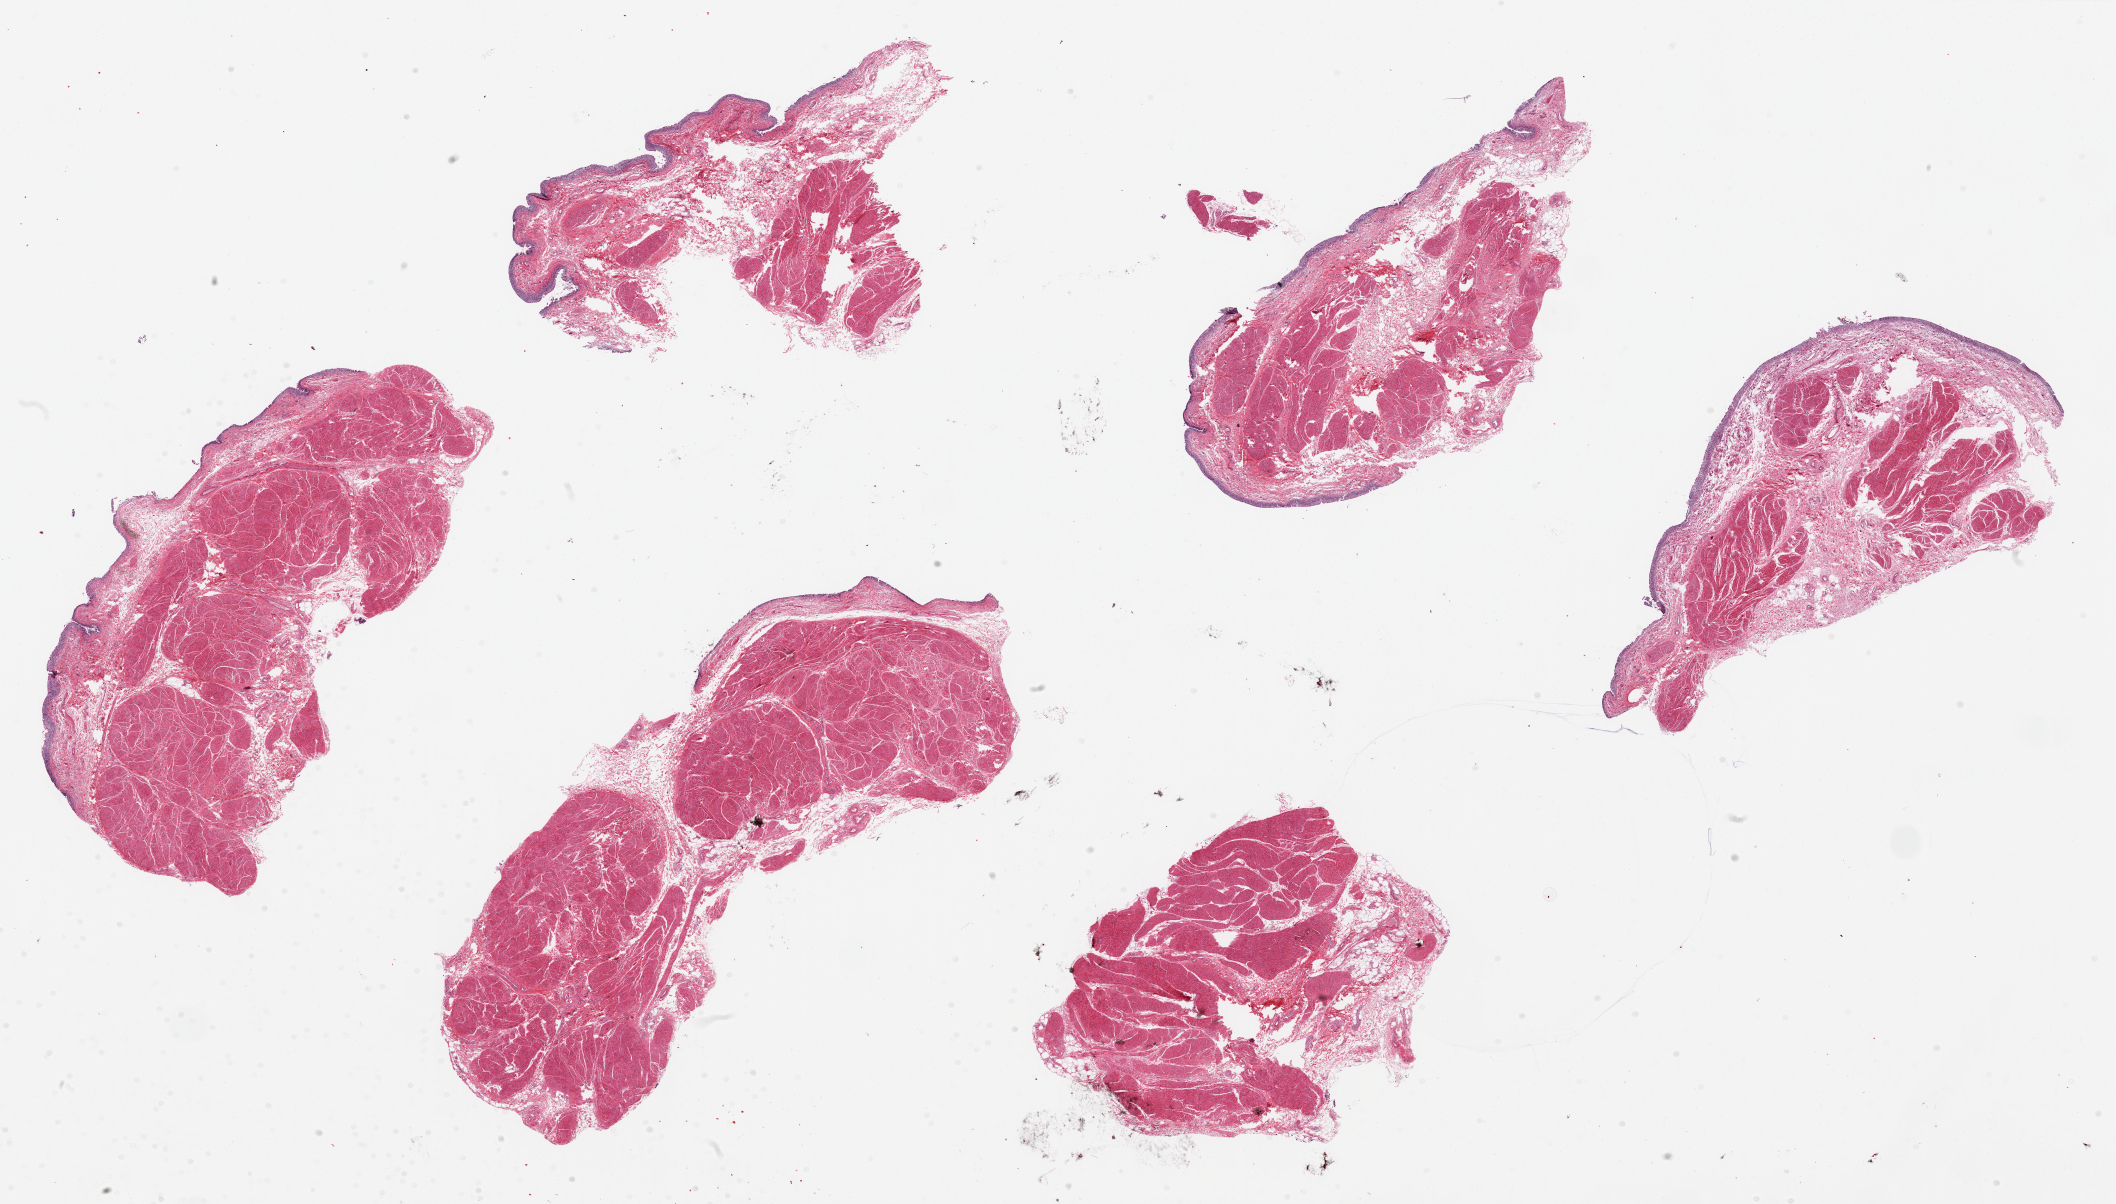
Whole-slide image, hematoxylin and eosin (H&E) stain, low-resolution overview of the scanned area, about 33.5 x 19.0 mm; PAXgene-fixed, paraffin-embedded tissue; sampled site (target tissue): urinary bladder; tissue donor sample. Male donor.
Pathologist's review note for this sample: 6 ~8x4 mm pieces, 4 with urothelium, reasonably well-preserved, ~2.5% of specimen thickness.